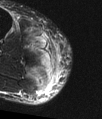
MRI of an extremity soft-tissue mass, one axial slice. Position 37 of 48 along the scan axis. T2-weighted fat-saturated. MR volume resampled by the dataset authors to the PET/CT grid (not the native acquisition matrix). 3.27 mm slice thickness. 102 × 119 image matrix, field of view 100 × 116 mm. Male patient. From the clinical record (not read from this slice): histological type: pleiomorphic liposarcoma; grade: high; site of the primary tumour: right calf.
Annotated regions visible in this slice (expert contour drawn on MRI and transferred to this co-registered scan by the dataset authors):
- gross tumour volume including surrounding oedema: bounding box [x1, y1, x2, y2] px = [46, 39, 58, 72]